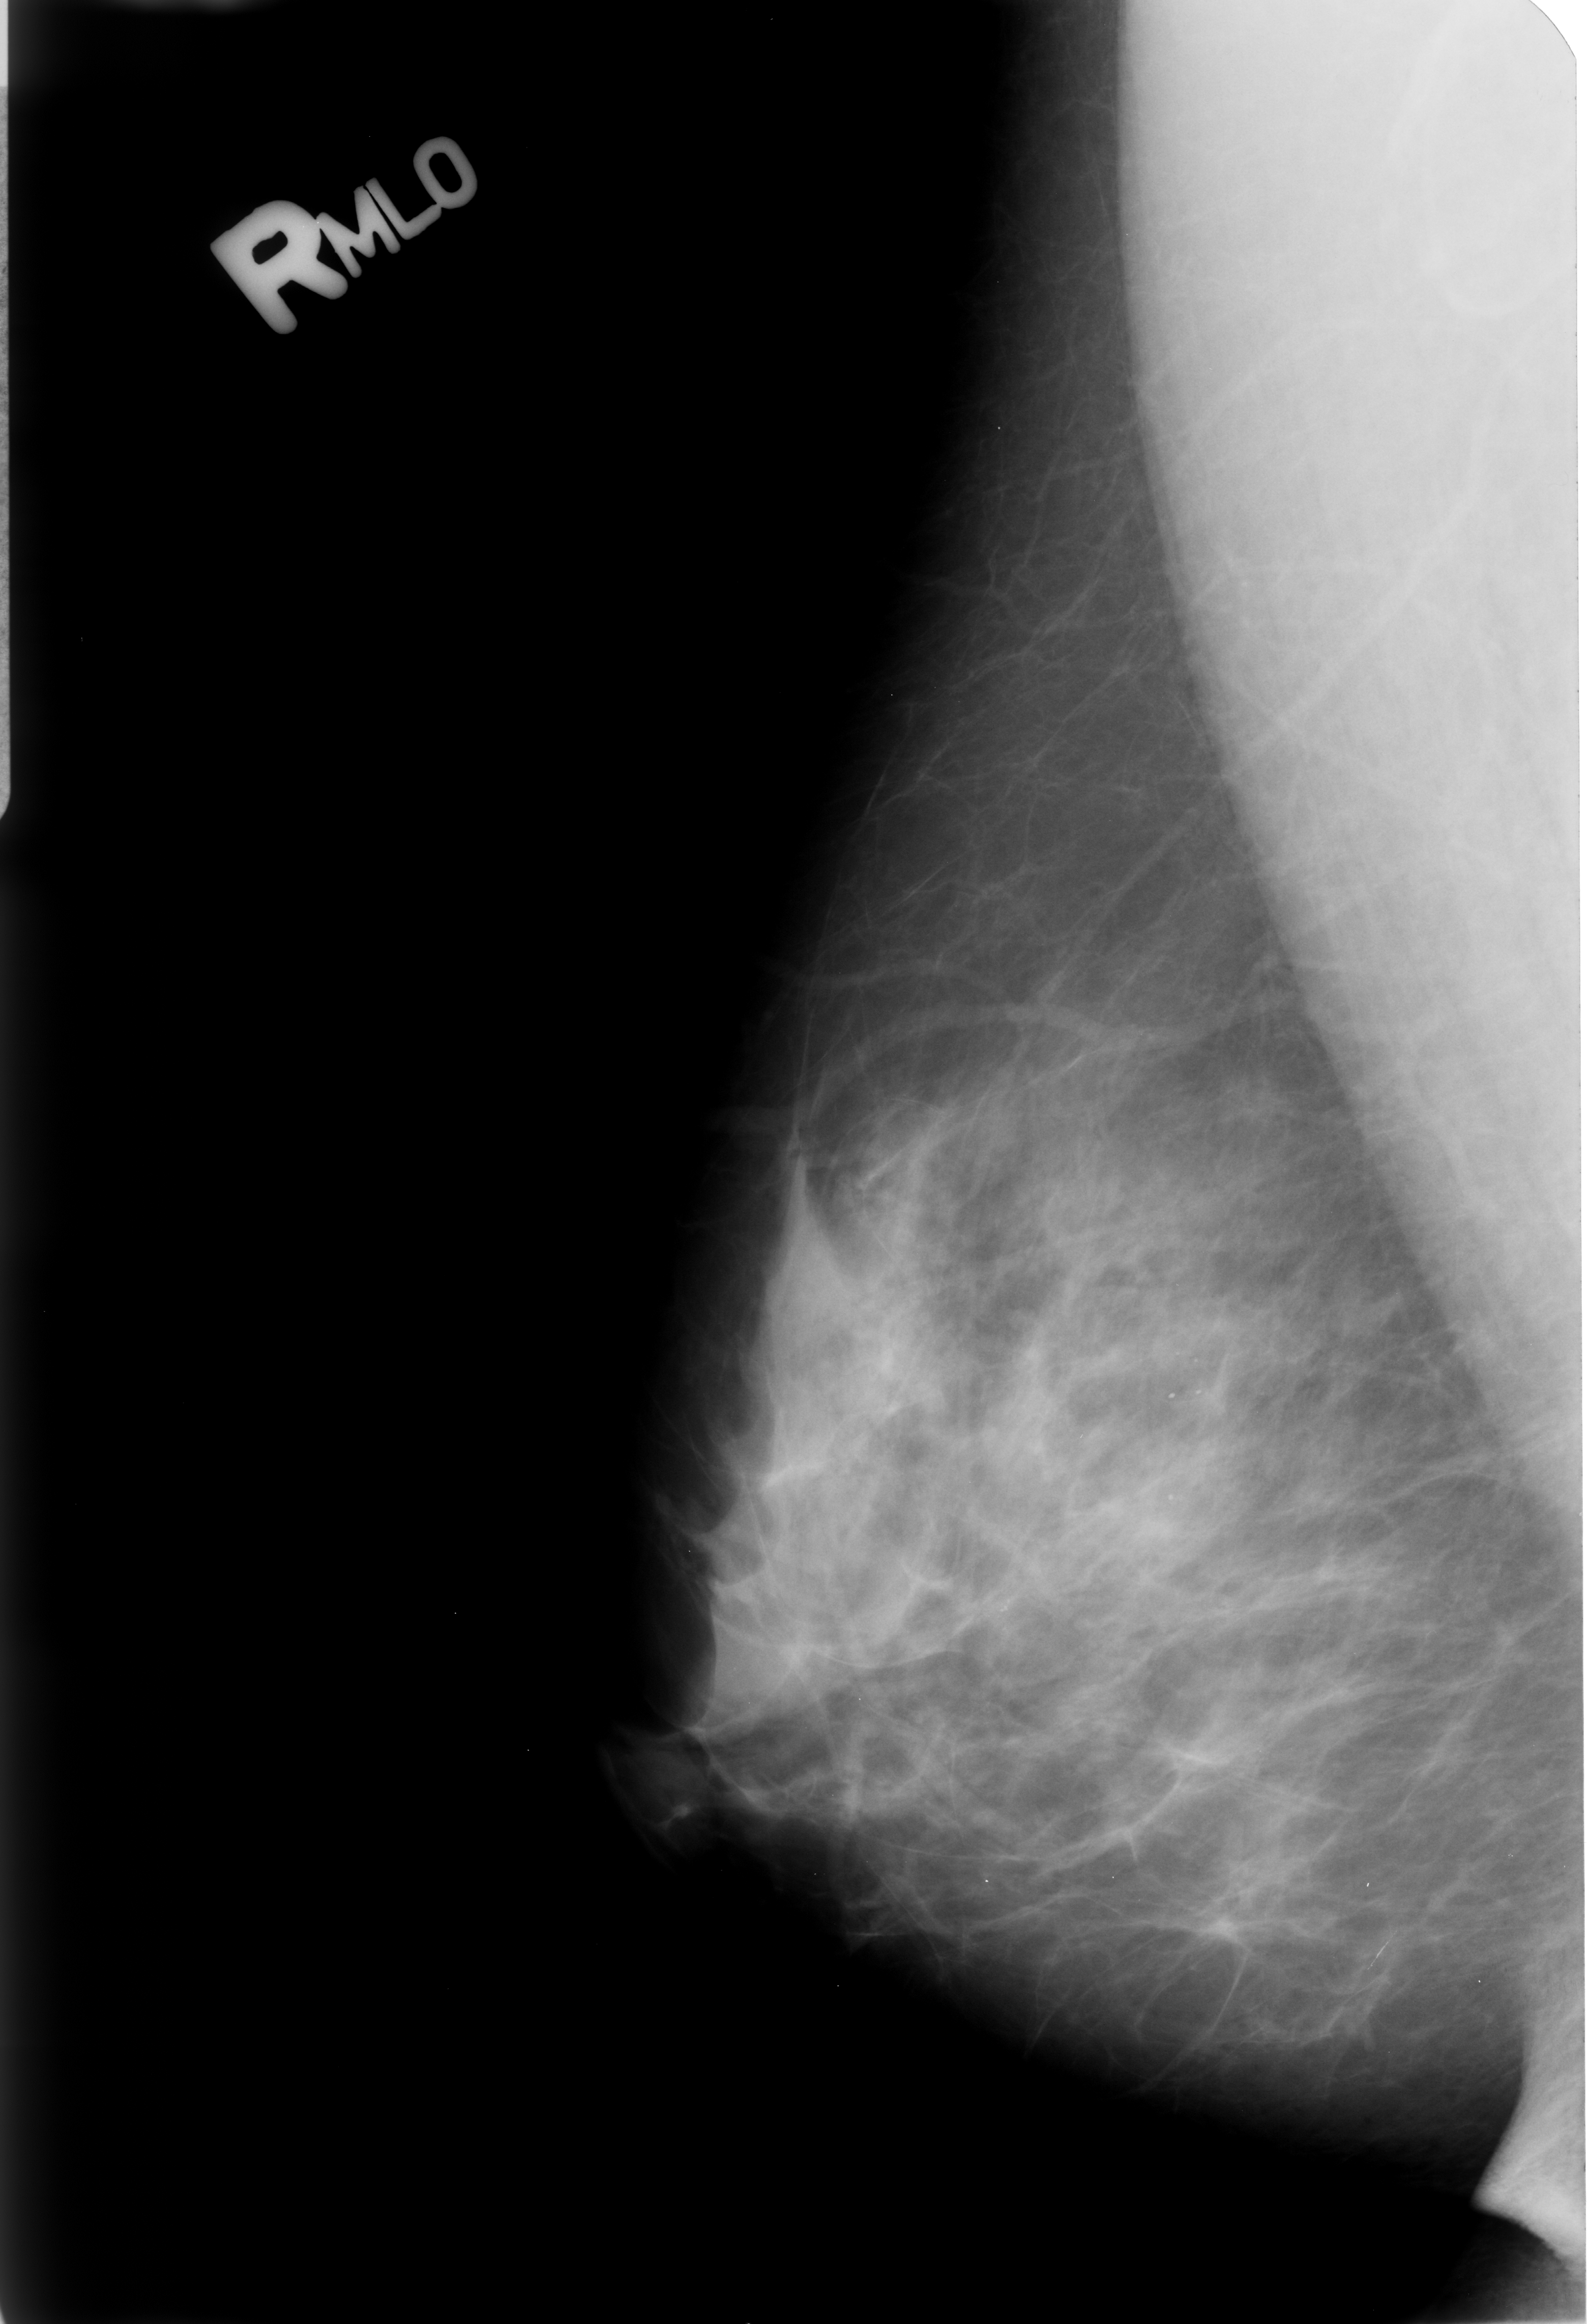
Digitized screen-film mammogram; right breast; MLO view; breast composition: heterogeneously dense (BI-RADS density category 3 of 4); 1587 × 2324 image matrix.
Expert-marked regions of interest on this film, with their recorded descriptors:
- Finding 1 of 2: calcifications, morphology punctate / round and regular, distribution regional; BI-RADS assessment category 2; outcome (as recorded, no biopsy): benign without callback (not worked up further): bounding box <992,1339,1067,1470> (left, top, right, bottom; pixels)
- Finding 2 of 2: calcifications, morphology punctate / round and regular, distribution regional; BI-RADS assessment category 2; outcome (as recorded, no biopsy): benign without callback (not worked up further): <1098,1155,1185,1283>